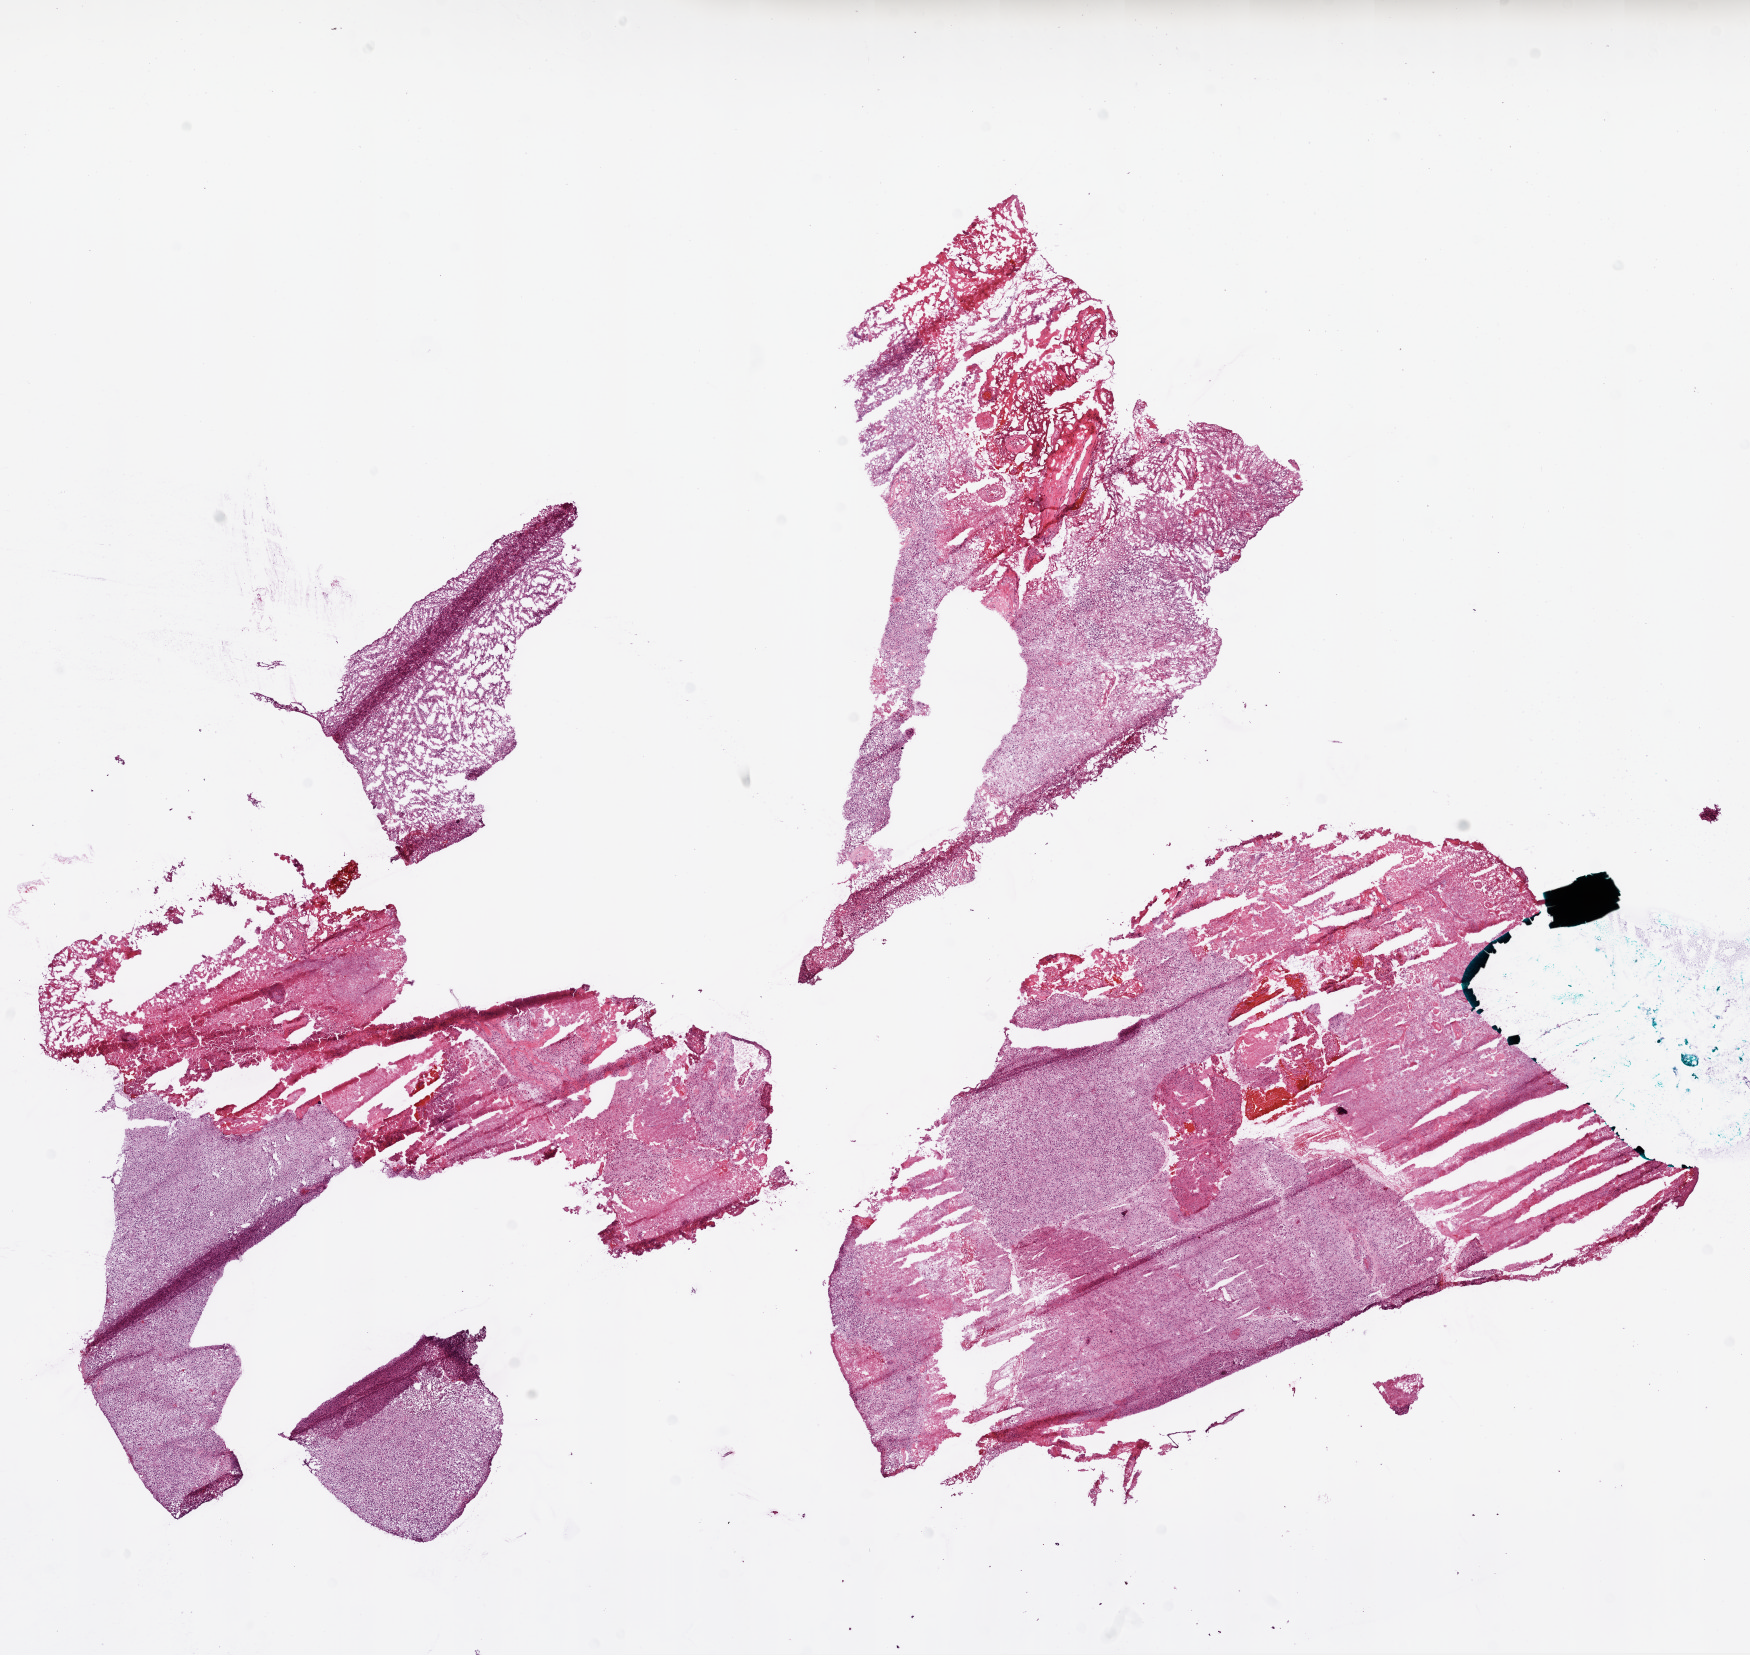
Whole-slide histology image, H&E, low-resolution overview of the scanned area, about 14.0 x 13.3 mm. Frozen section from the bottom of the tissue portion. Brain, primary tumour sample. Female patient; age at initial diagnosis 58 years. Pathologist review of this section (percent, as recorded): tumour cells 90%, tumour nuclei 95%, stromal cells 5%, necrosis 5%.
• diagnosis: Glioblastoma